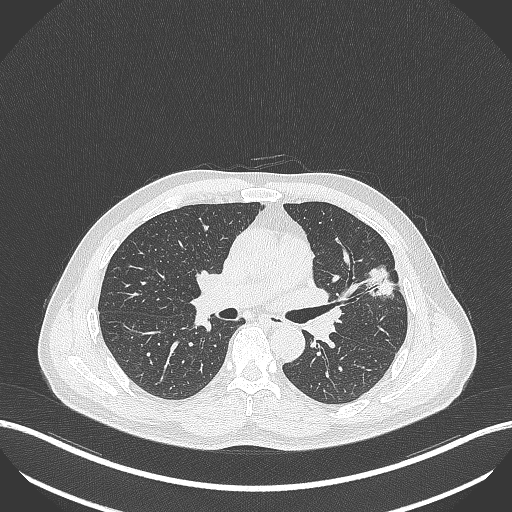
Chest CT, one axial slice. Position 226 of 418 along the scan axis. Reconstruction kernel B70f. Lung window (W 1500 / L -600 HU). 1 mm slice thickness. 512 × 512 image matrix, field of view 400 × 400 mm. Patient: male, 55 years. Case-level facts recorded for this patient, not image findings: clinical TNM (as recorded): T1c N0 M0.
Annotated regions visible in this slice (bounding box drawn by a radiologist):
- lung tumour (recorded histology: adenocarcinoma): bounding box (x1, y1, x2, y2) in pixels: (364, 264, 400, 301)